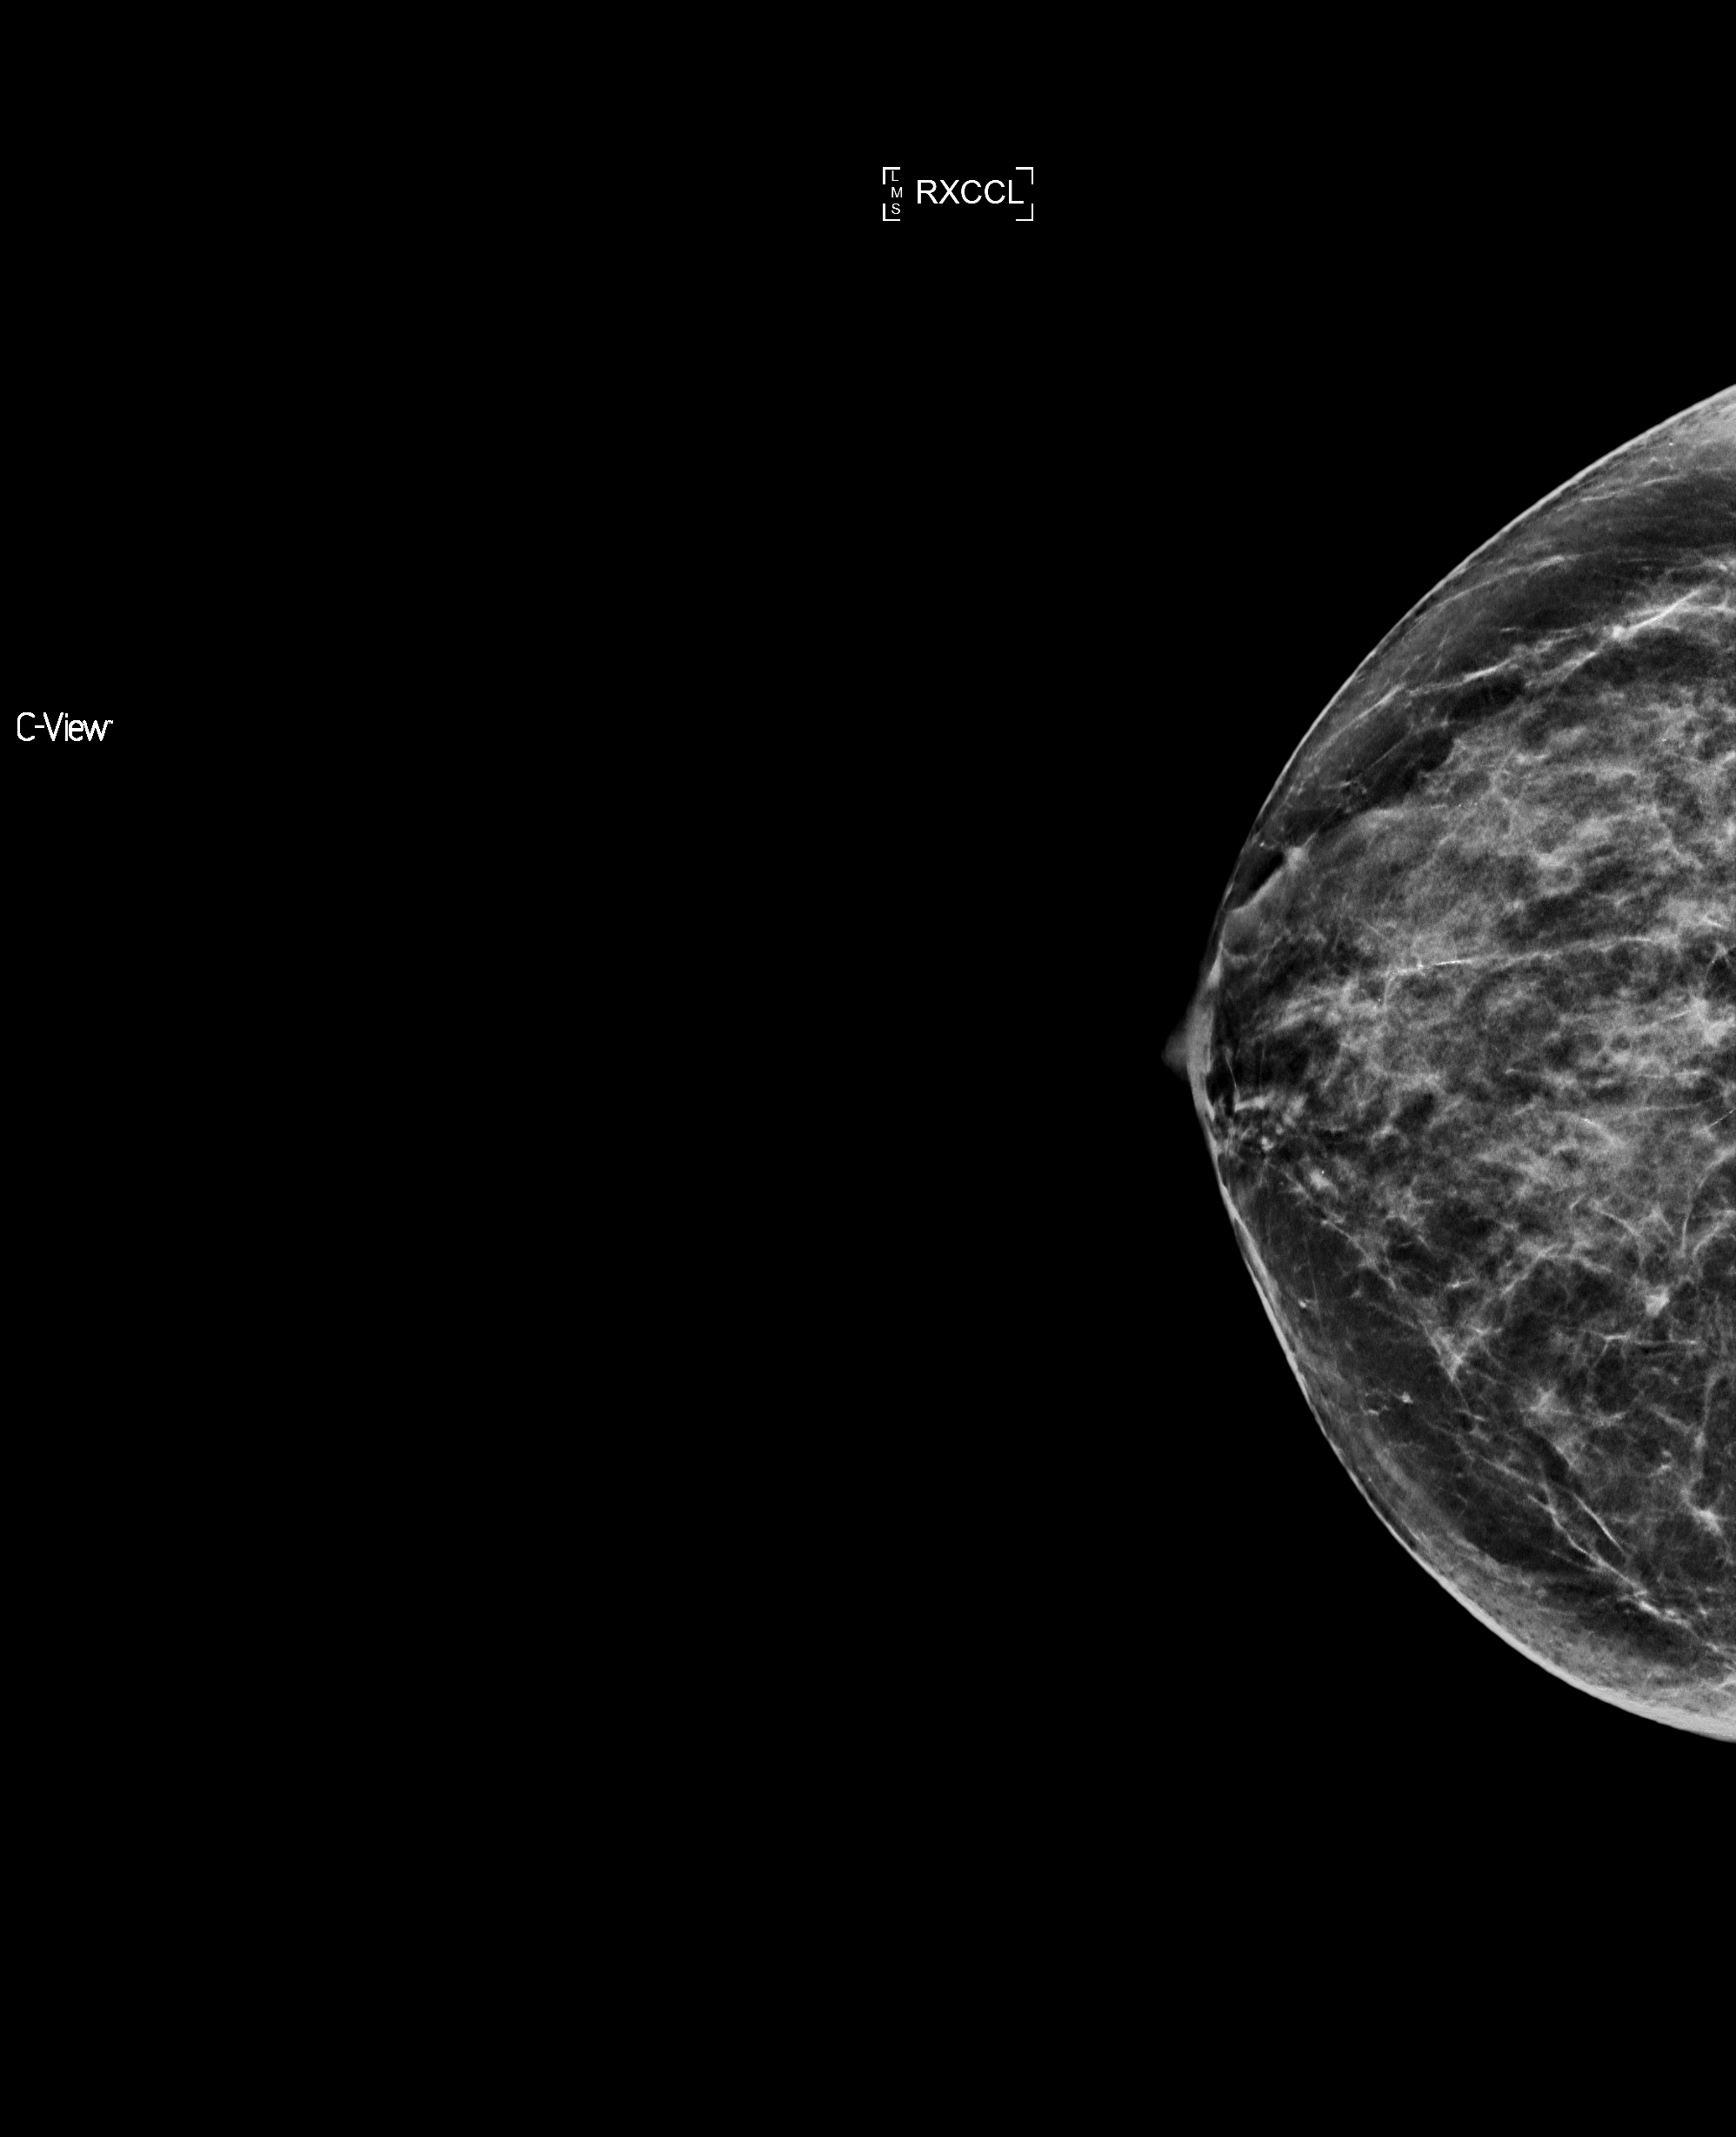
Digital mammogram (FFDM), right breast, laterally exaggerated craniocaudal (XCCL) view, screening examination, compressed breast thickness 52 mm. Female patient, age 59 years.
- BI-RADS breast density category at the screening exam (both breasts, scale 1–4): 3
- final BI-RADS category for the screening round (tomosynthesis exam, both breasts): category 1
- recall: no recall after this screen